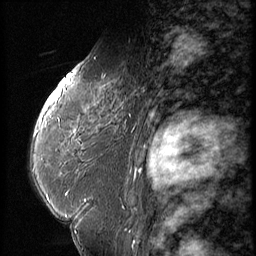
Breast MRI (dynamic contrast-enhanced), one sagittal slice. Slice 36 of 56 in the series (ordered by position). Dynamic contrast-enhanced series, image 2 of 3 at this slice position (ordered by acquisition). 1.5 T. TE 4.2 ms, TR 9 ms. 256 × 256 image matrix, field of view 180 × 180 mm. Patient: female, 59 years. From the clinical record (not read from this slice): setting: breast cancer imaged before/during neoadjuvant chemotherapy; receptor status: HER2-positive.
Structures marked on this image (semi-automatic segmentation, software-assisted and operator-edited):
- analysis volume of interest (the breast-tissue region the enhancement analysis was run in; not a lesion): bounding box <44,66,151,135> (left, top, right, bottom; pixels)
- tumour enhancement mask (voxels above the 140 % enhancement threshold inside the analysis volume of interest): <45,73,73,107>